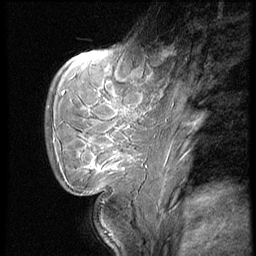
Breast MRI (dynamic contrast-enhanced), one sagittal slice; slice 17 of 62 in the series (ordered by position); dynamic contrast-enhanced series, image 2 of 4 at this slice position (ordered by acquisition); 1.5 T; TE 4.2 ms, TR 9 ms; 2.5 mm slice thickness; 256 × 256 image matrix, field of view 180 × 180 mm. Patient: female, 28 years. Case-level facts recorded for this patient, not image findings: setting: breast cancer imaged before/during neoadjuvant chemotherapy.
Annotated regions visible in this slice (semi-automatically segmented with operator editing):
- analysis volume of interest (the breast-tissue region the enhancement analysis was run in; not a lesion): box from (x=48, y=54) to (x=150, y=183) px
- tumour enhancement mask (voxels above the 140 % enhancement threshold inside the analysis volume of interest): (x=89, y=163)–(x=124, y=170)